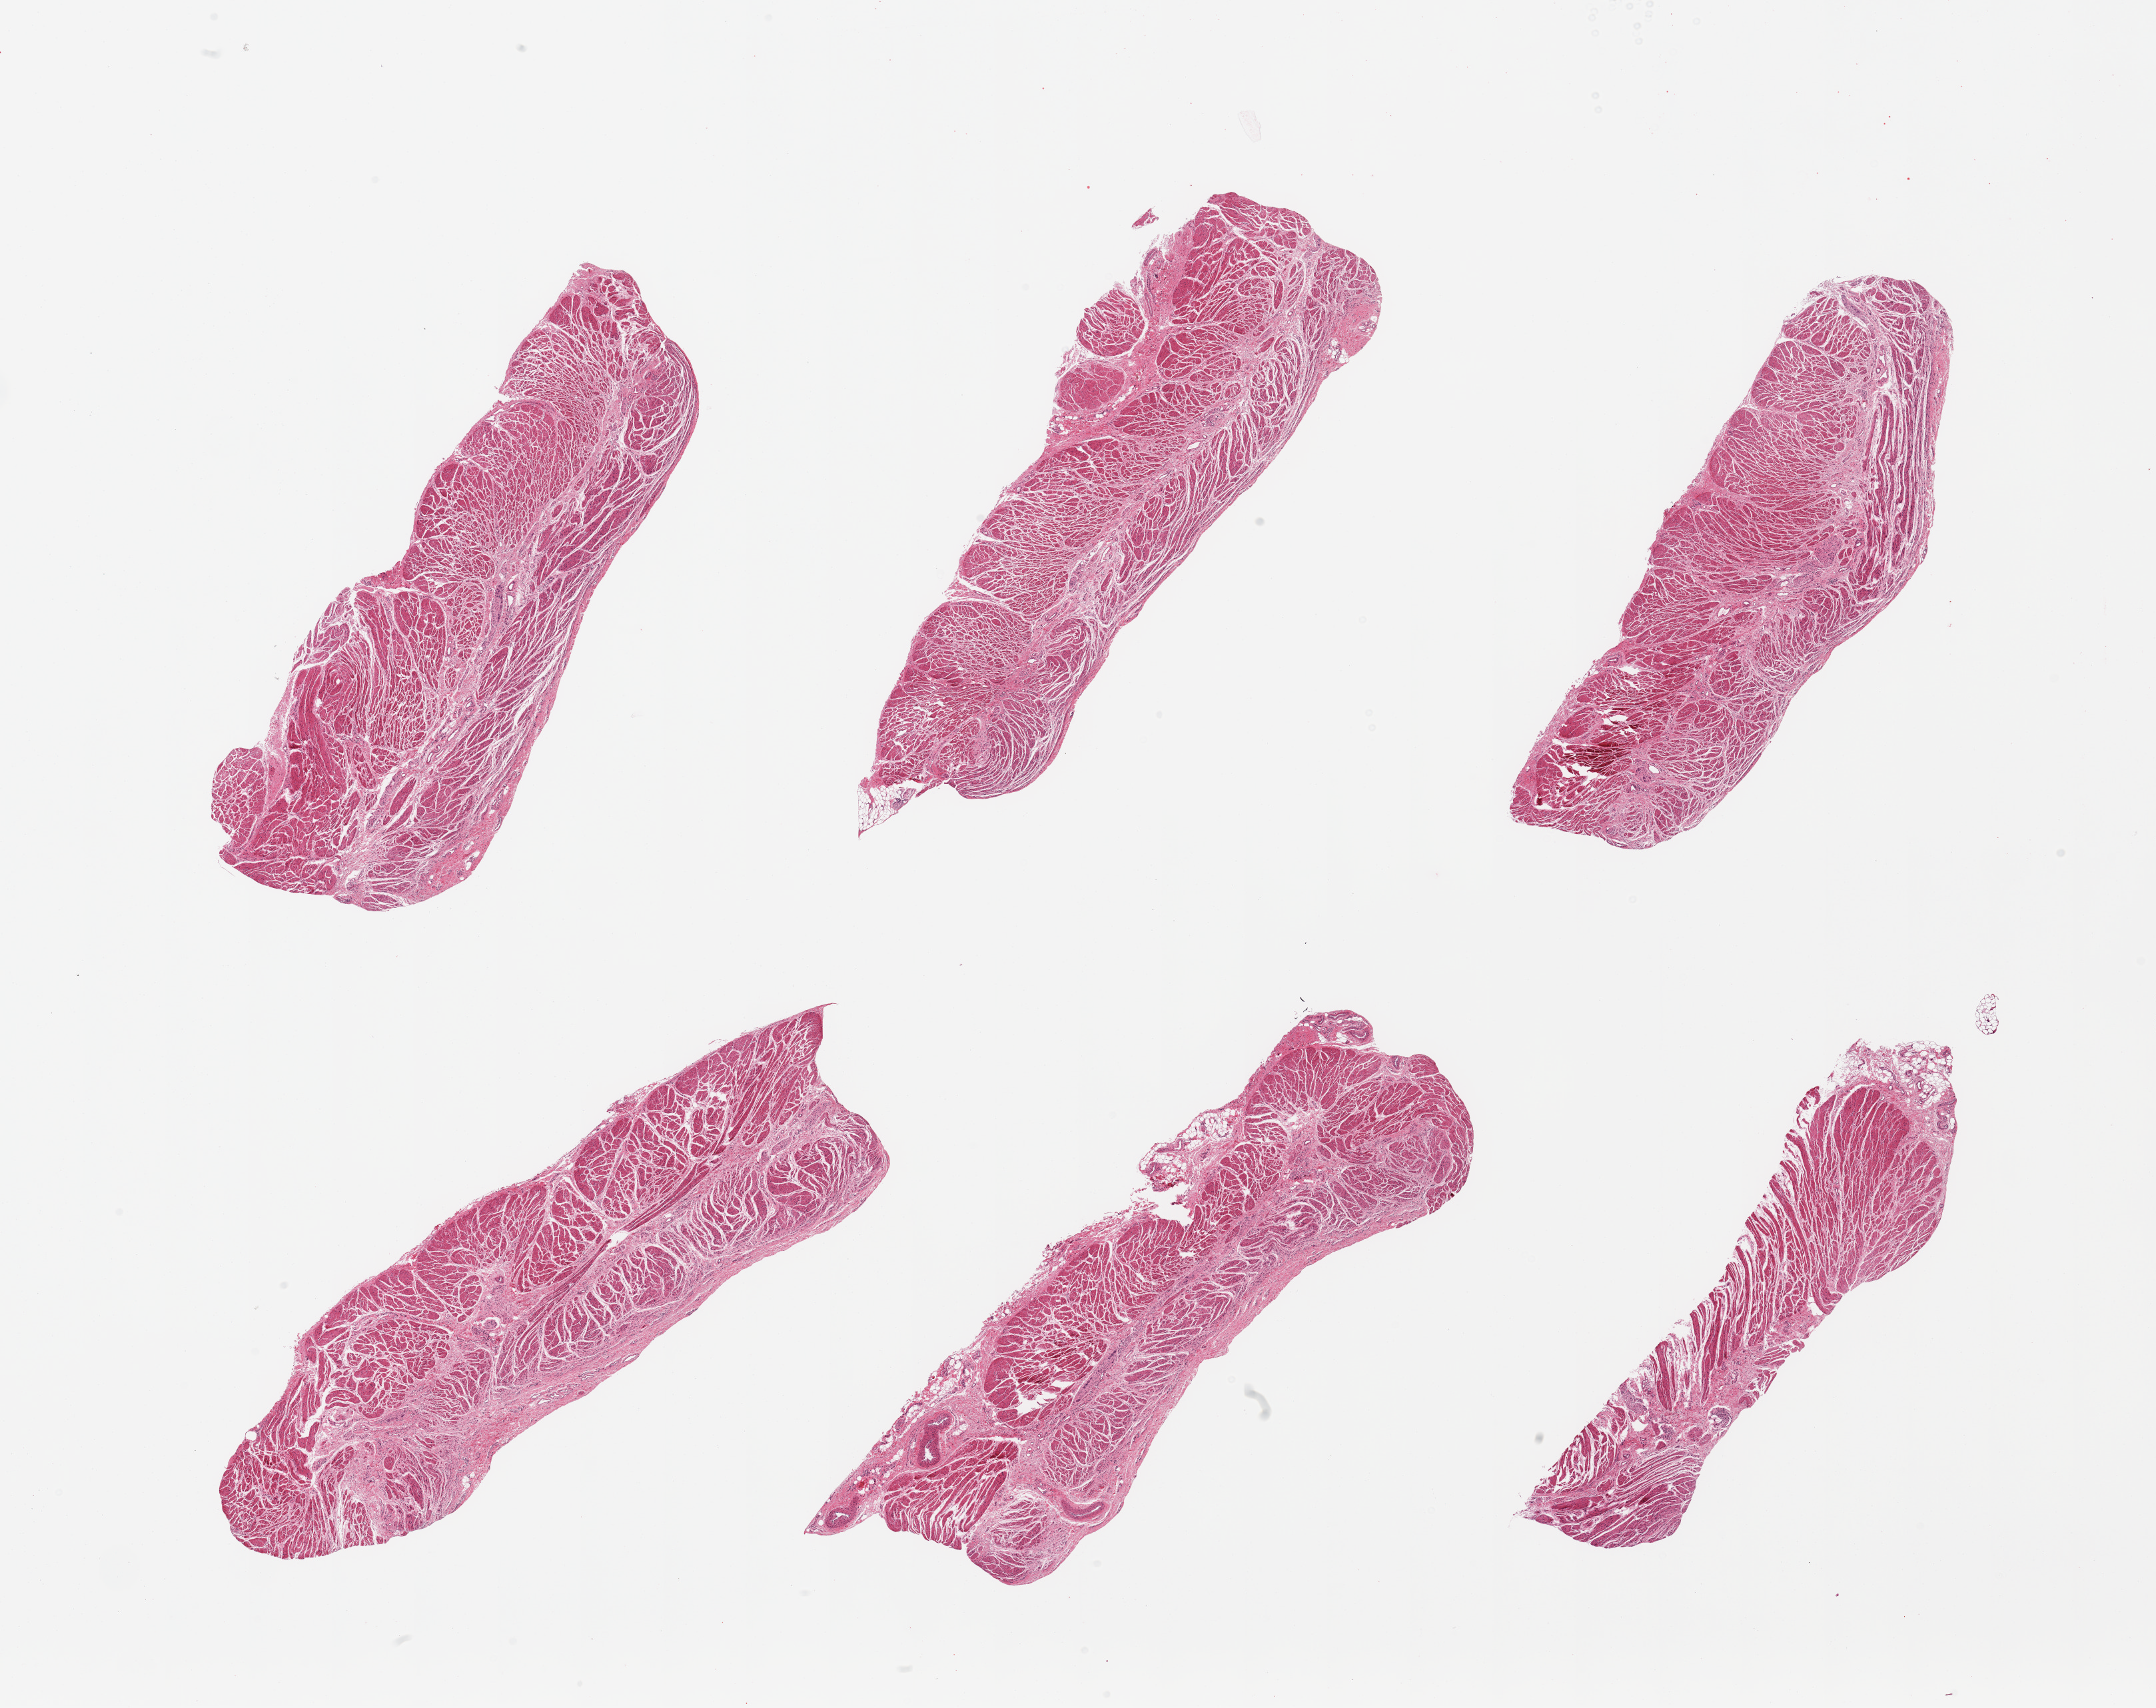
Whole-slide image, hematoxylin and eosin (H&E) stain, whole scanned area (about 25.6 x 20.3 mm) shown as a low-resolution overview, PAXgene-fixed, paraffin-embedded tissue, section of gastroesophageal junction (target tissue), tissue donor sample. Donor: male.
* pathologist's review note for this sample: 6 pieces; well trimmed